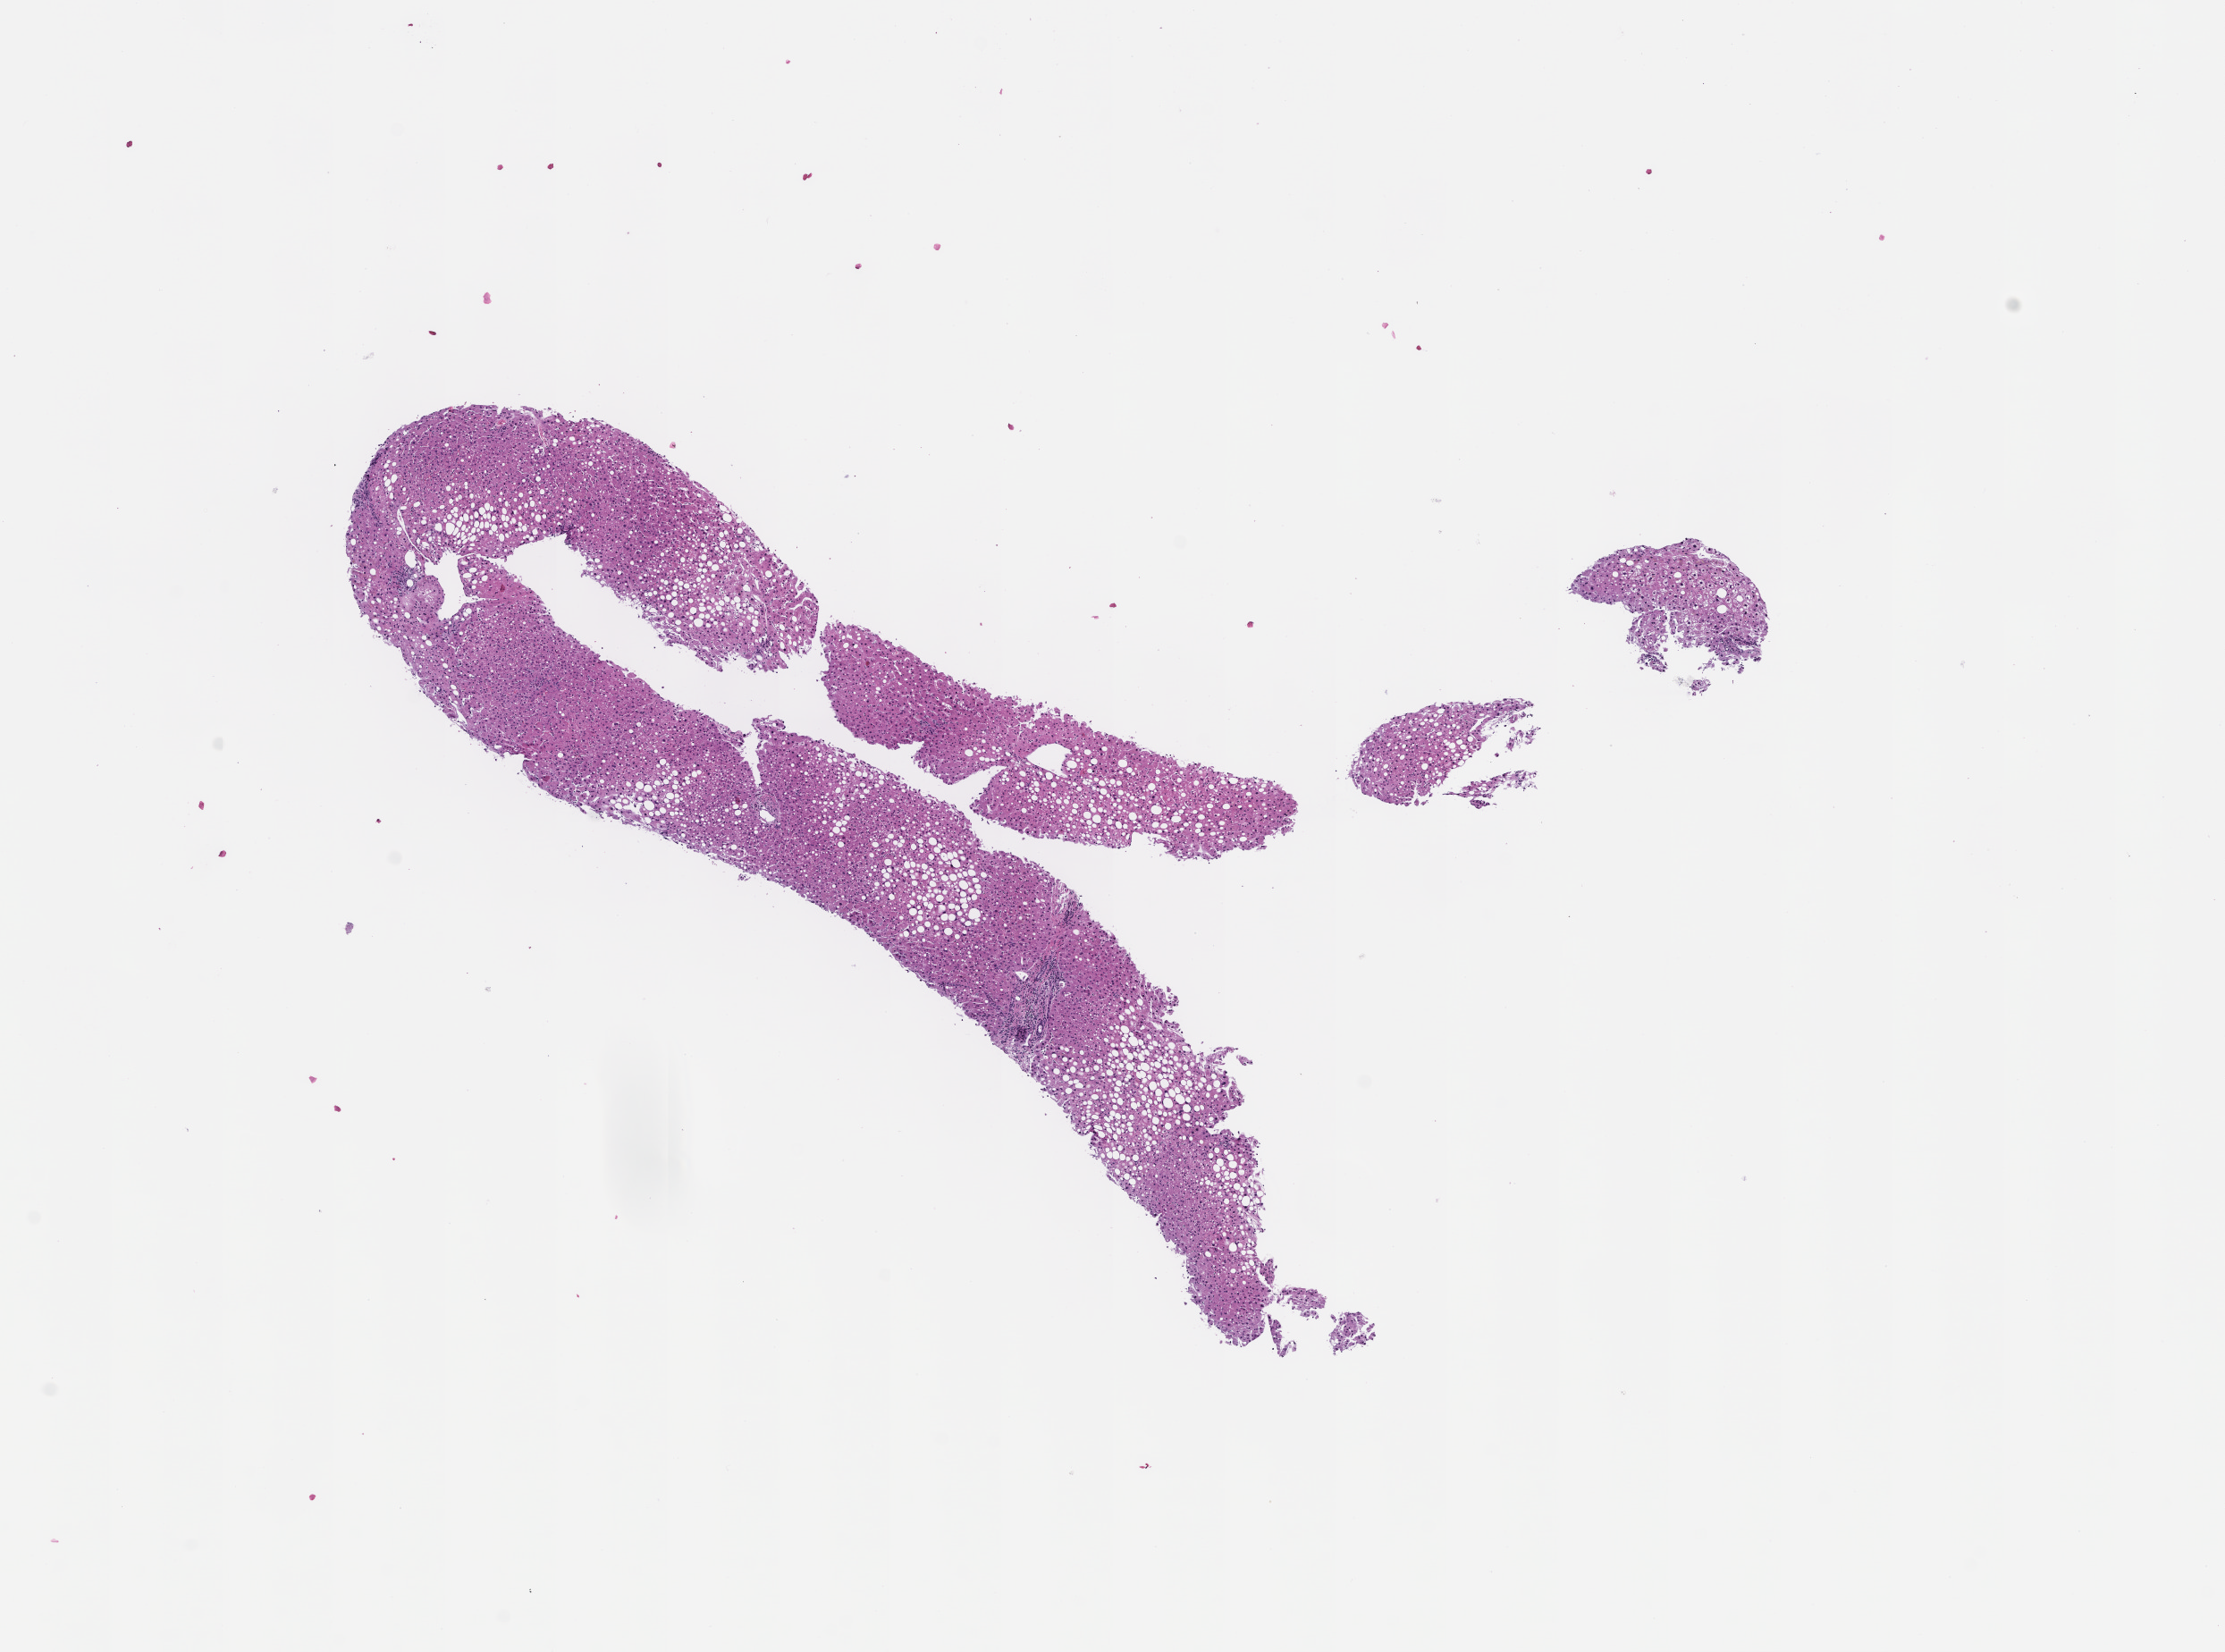
Whole-slide image, hematoxylin and eosin (H&E) stain — a low-resolution overview of the entire scanned area, about 10.1 x 7.5 mm, FFPE section, collected at baseline (before treatment). Patient sex: male.
This section: metastatic tumor tissue. Primary diagnosis of the patient: Melanoma.